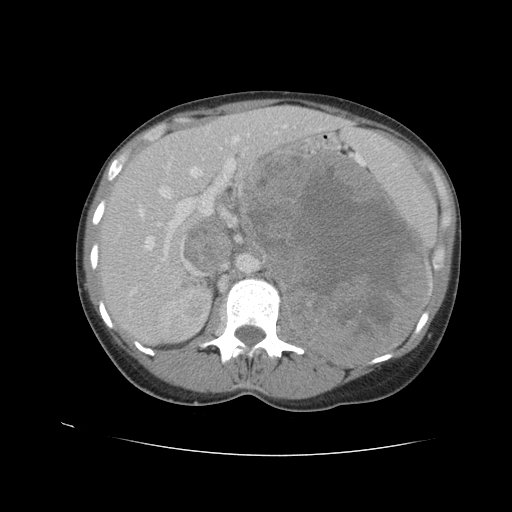
Contrast-enhanced abdominal CT, one axial slice. Reconstruction kernel STANDARD. 120 kVp. Intravenous contrast given. Soft-tissue window (W 400 / L 40 HU). 512 × 512 image matrix. Female patient. From the clinical record (not read from this slice): diagnosis: adrenocortical carcinoma; tumour side: left adrenal; tumour size at pathology: 18 cm; Ki-67 index: 11 %; stage (as recorded): 3.
Outlined on this slice (semi-automatically segmented with operator editing):
- mass: bounding box (x1, y1, x2, y2) in pixels: (246, 153, 427, 363)